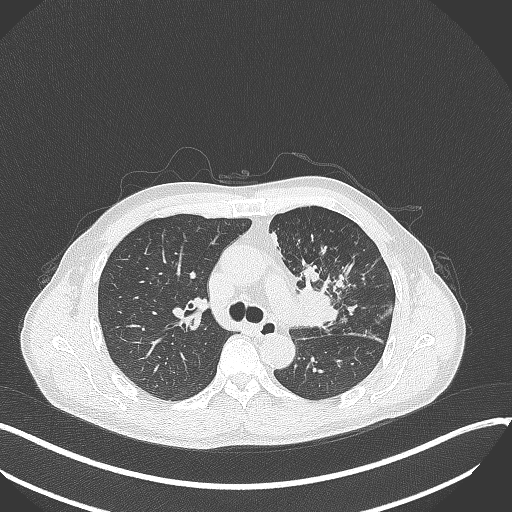
Chest CT, one axial slice. Slice 223 of 411 in the series (ordered by position). Reconstruction kernel B70f. 120 kVp. Lung window (W 1500 / L -600 HU). 512 × 512 image matrix, field of view 400 × 400 mm. Patient: male, 56 years. From the clinical record (not read from this slice): clinical TNM (as recorded): T2a N0 M0.
Outlined on this slice (bounding box drawn by a radiologist):
- lung tumour (recorded histology: squamous cell carcinoma): bounding box <294,281,340,334> (left, top, right, bottom; pixels)